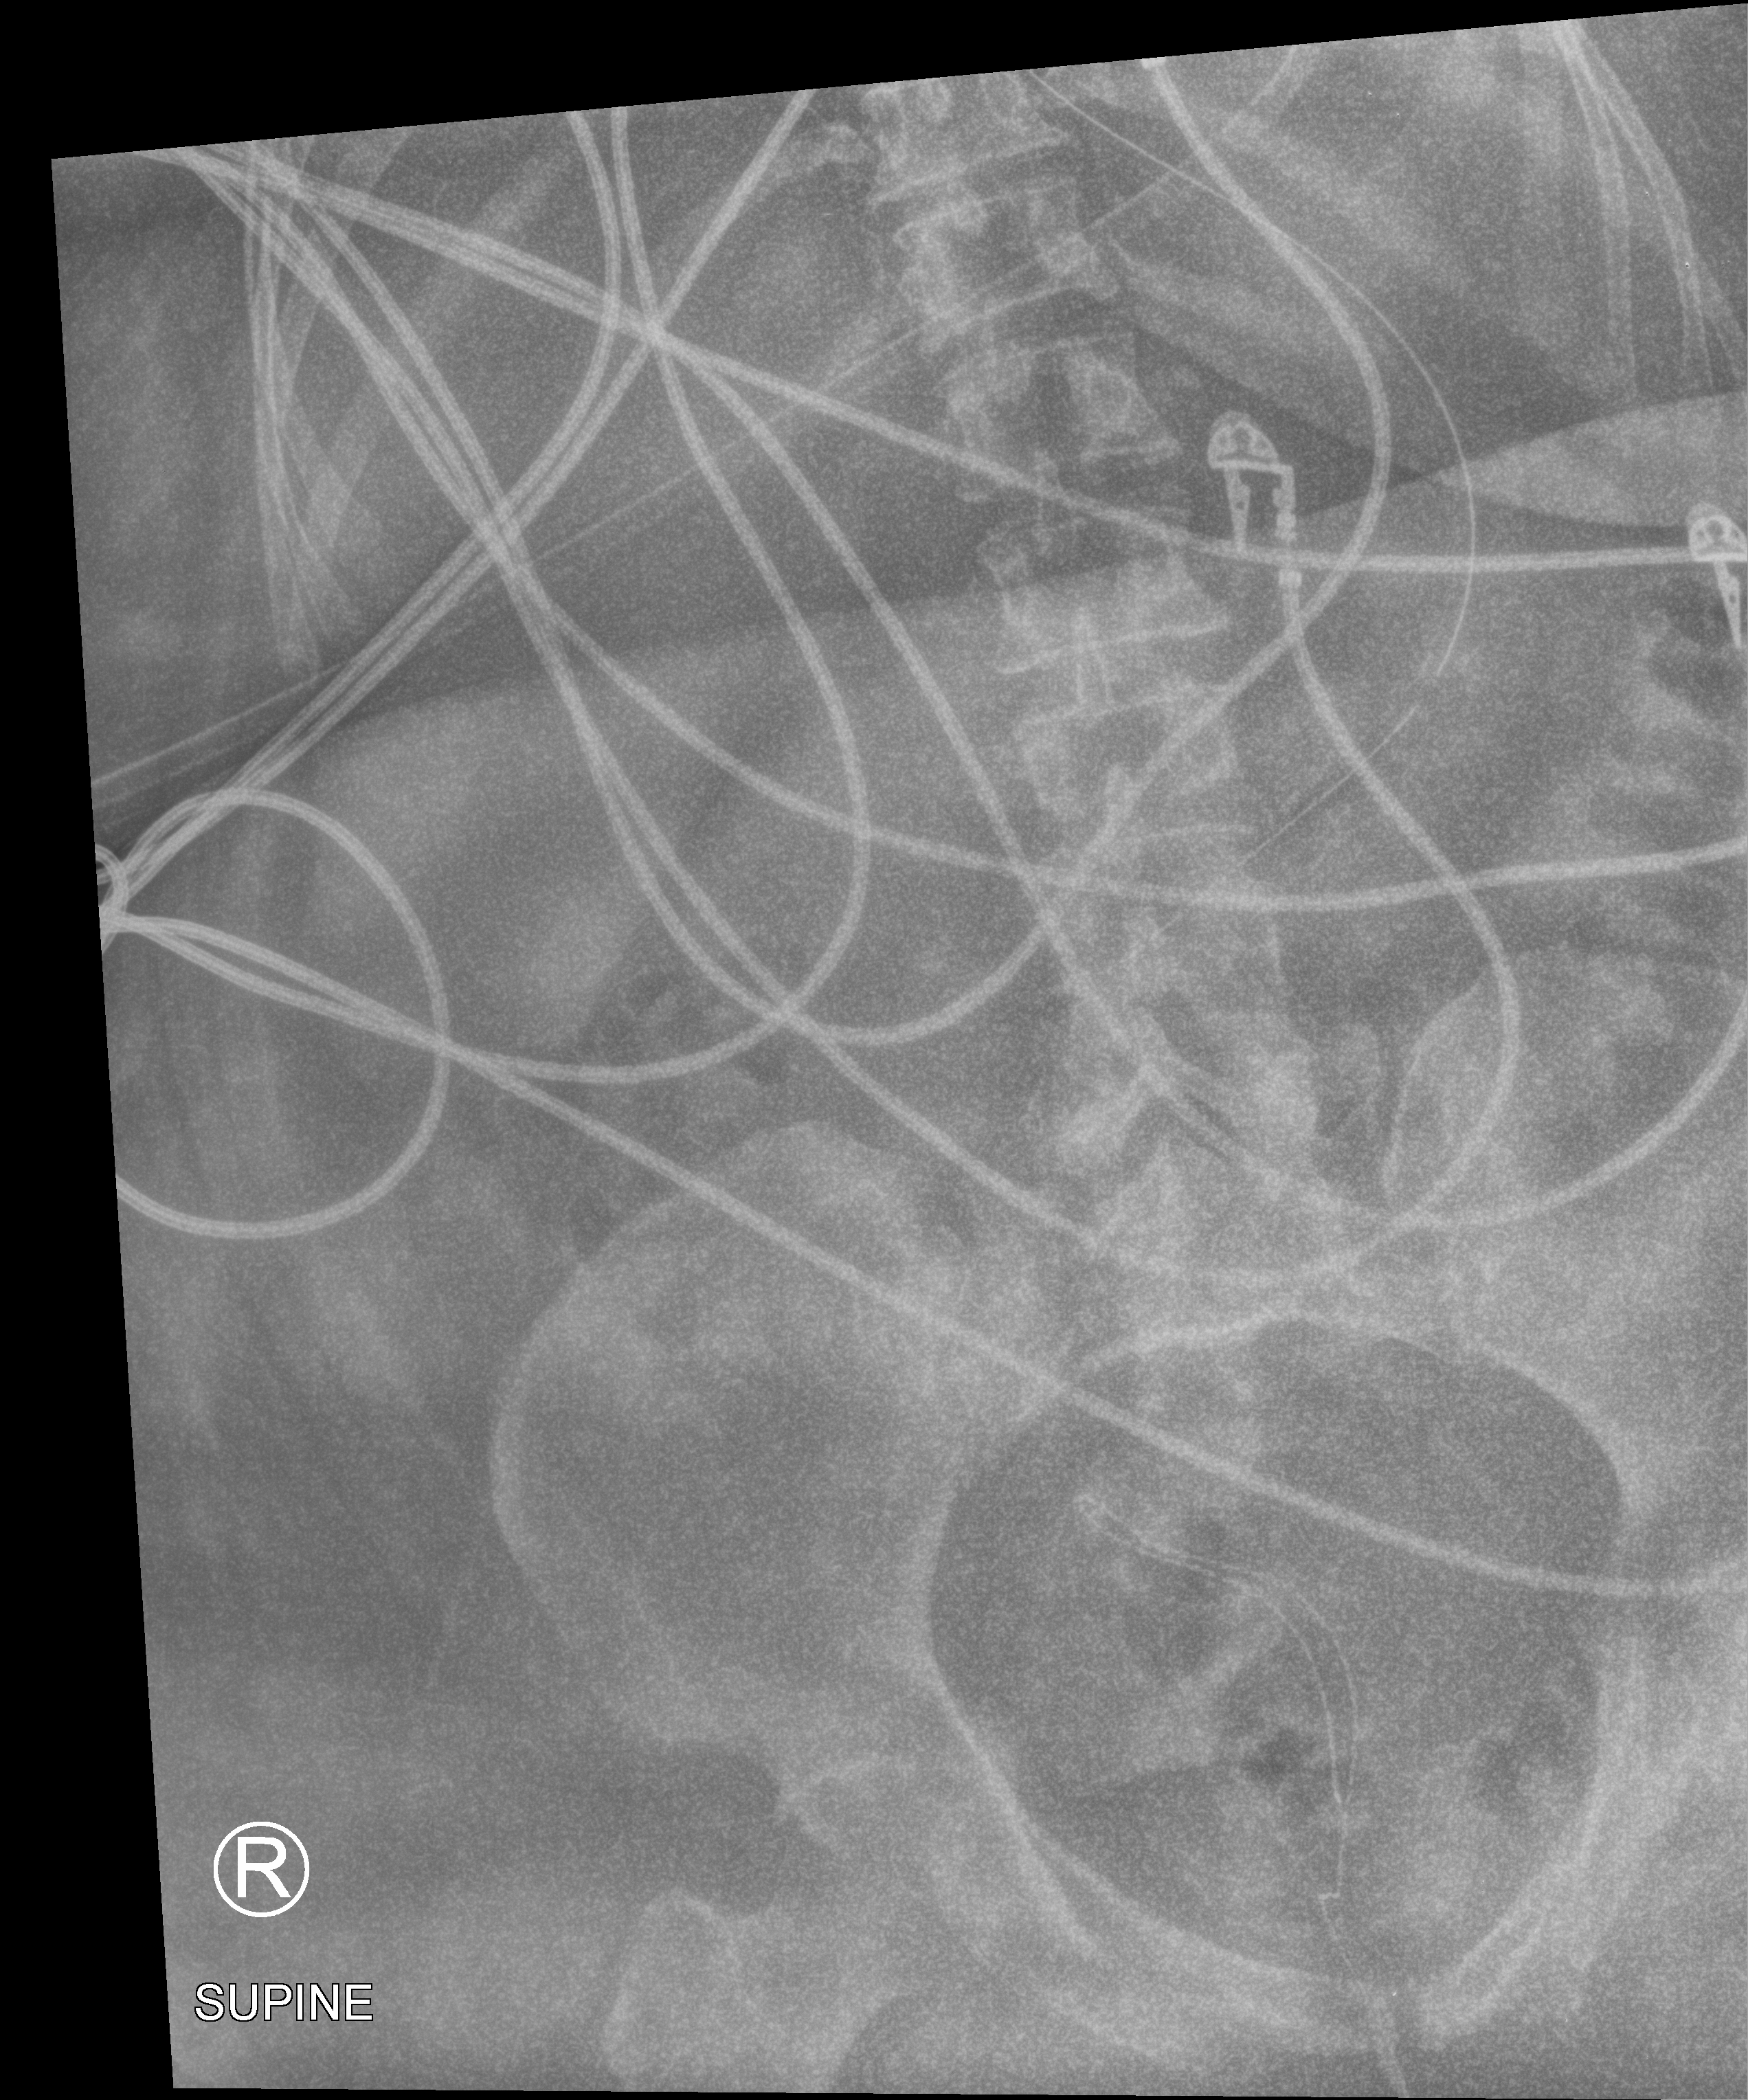
Abdomen X-ray (portable); anteroposterior (AP) projection. Female patient hospitalised with COVID-19, age 18–59 years.
From the hospital-stay record, not from the radiograph (when in the stay this image was taken is not recorded): admitted to intensive care during this hospital stay: yes; mechanically ventilated during this hospital stay: yes; chronic kidney disease (admission record): no.